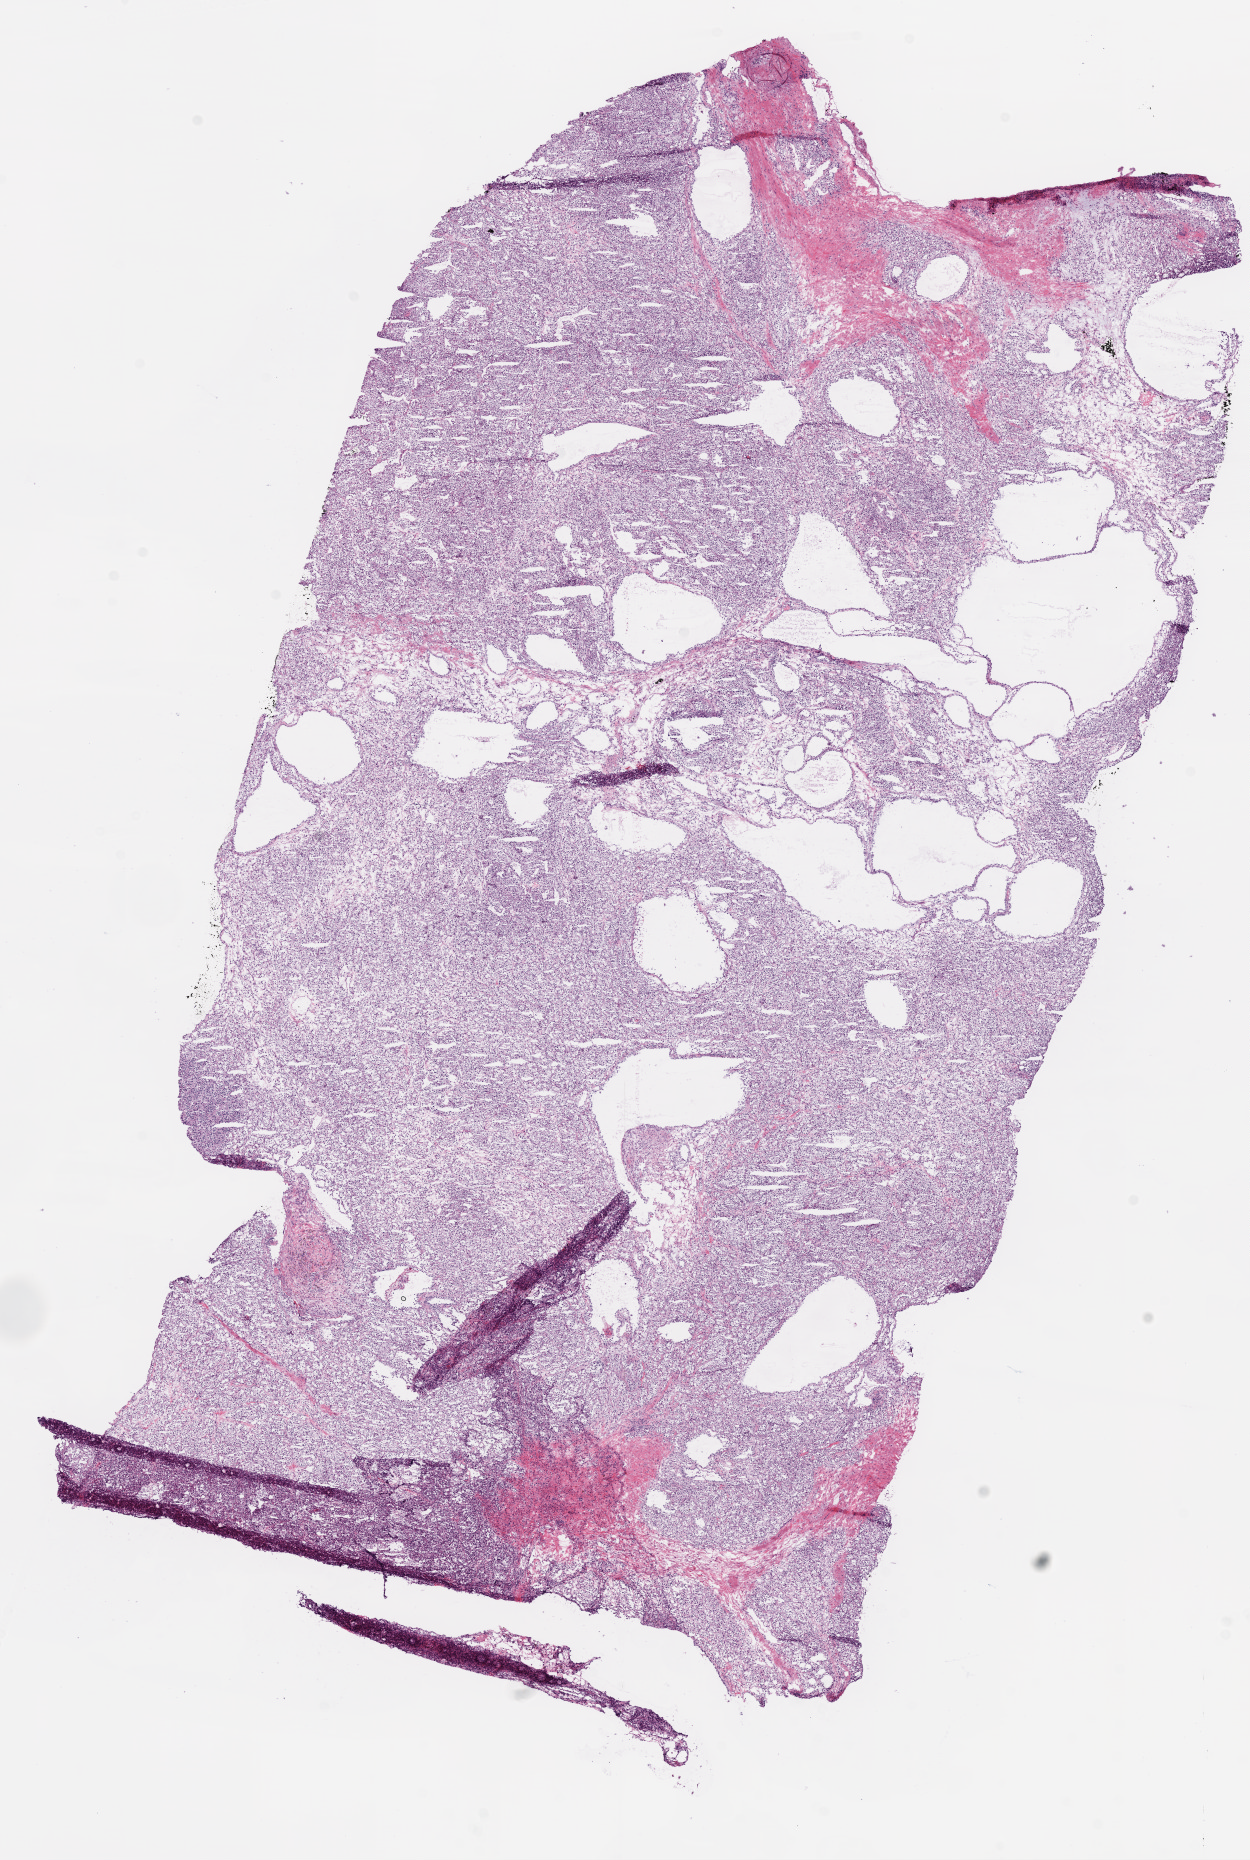
H&E-stained whole-slide image, whole scanned area (about 10.0 x 14.9 mm, slide scanned at 20x) shown as a low-resolution overview. Frozen section. Sample: primary tumour, kidney. Male, age 51 years at initial diagnosis. Histologic grade: G2 (moderately differentiated). Pathologist review of this section (percent, as recorded): tumour cells 85%, tumour nuclei 85%, normal cells 10%, stromal cells 5%, necrosis 0%.
Histologic diagnosis: Clear cell adenocarcinoma, NOS. AJCC pathologic stage: I. Laterality: left.